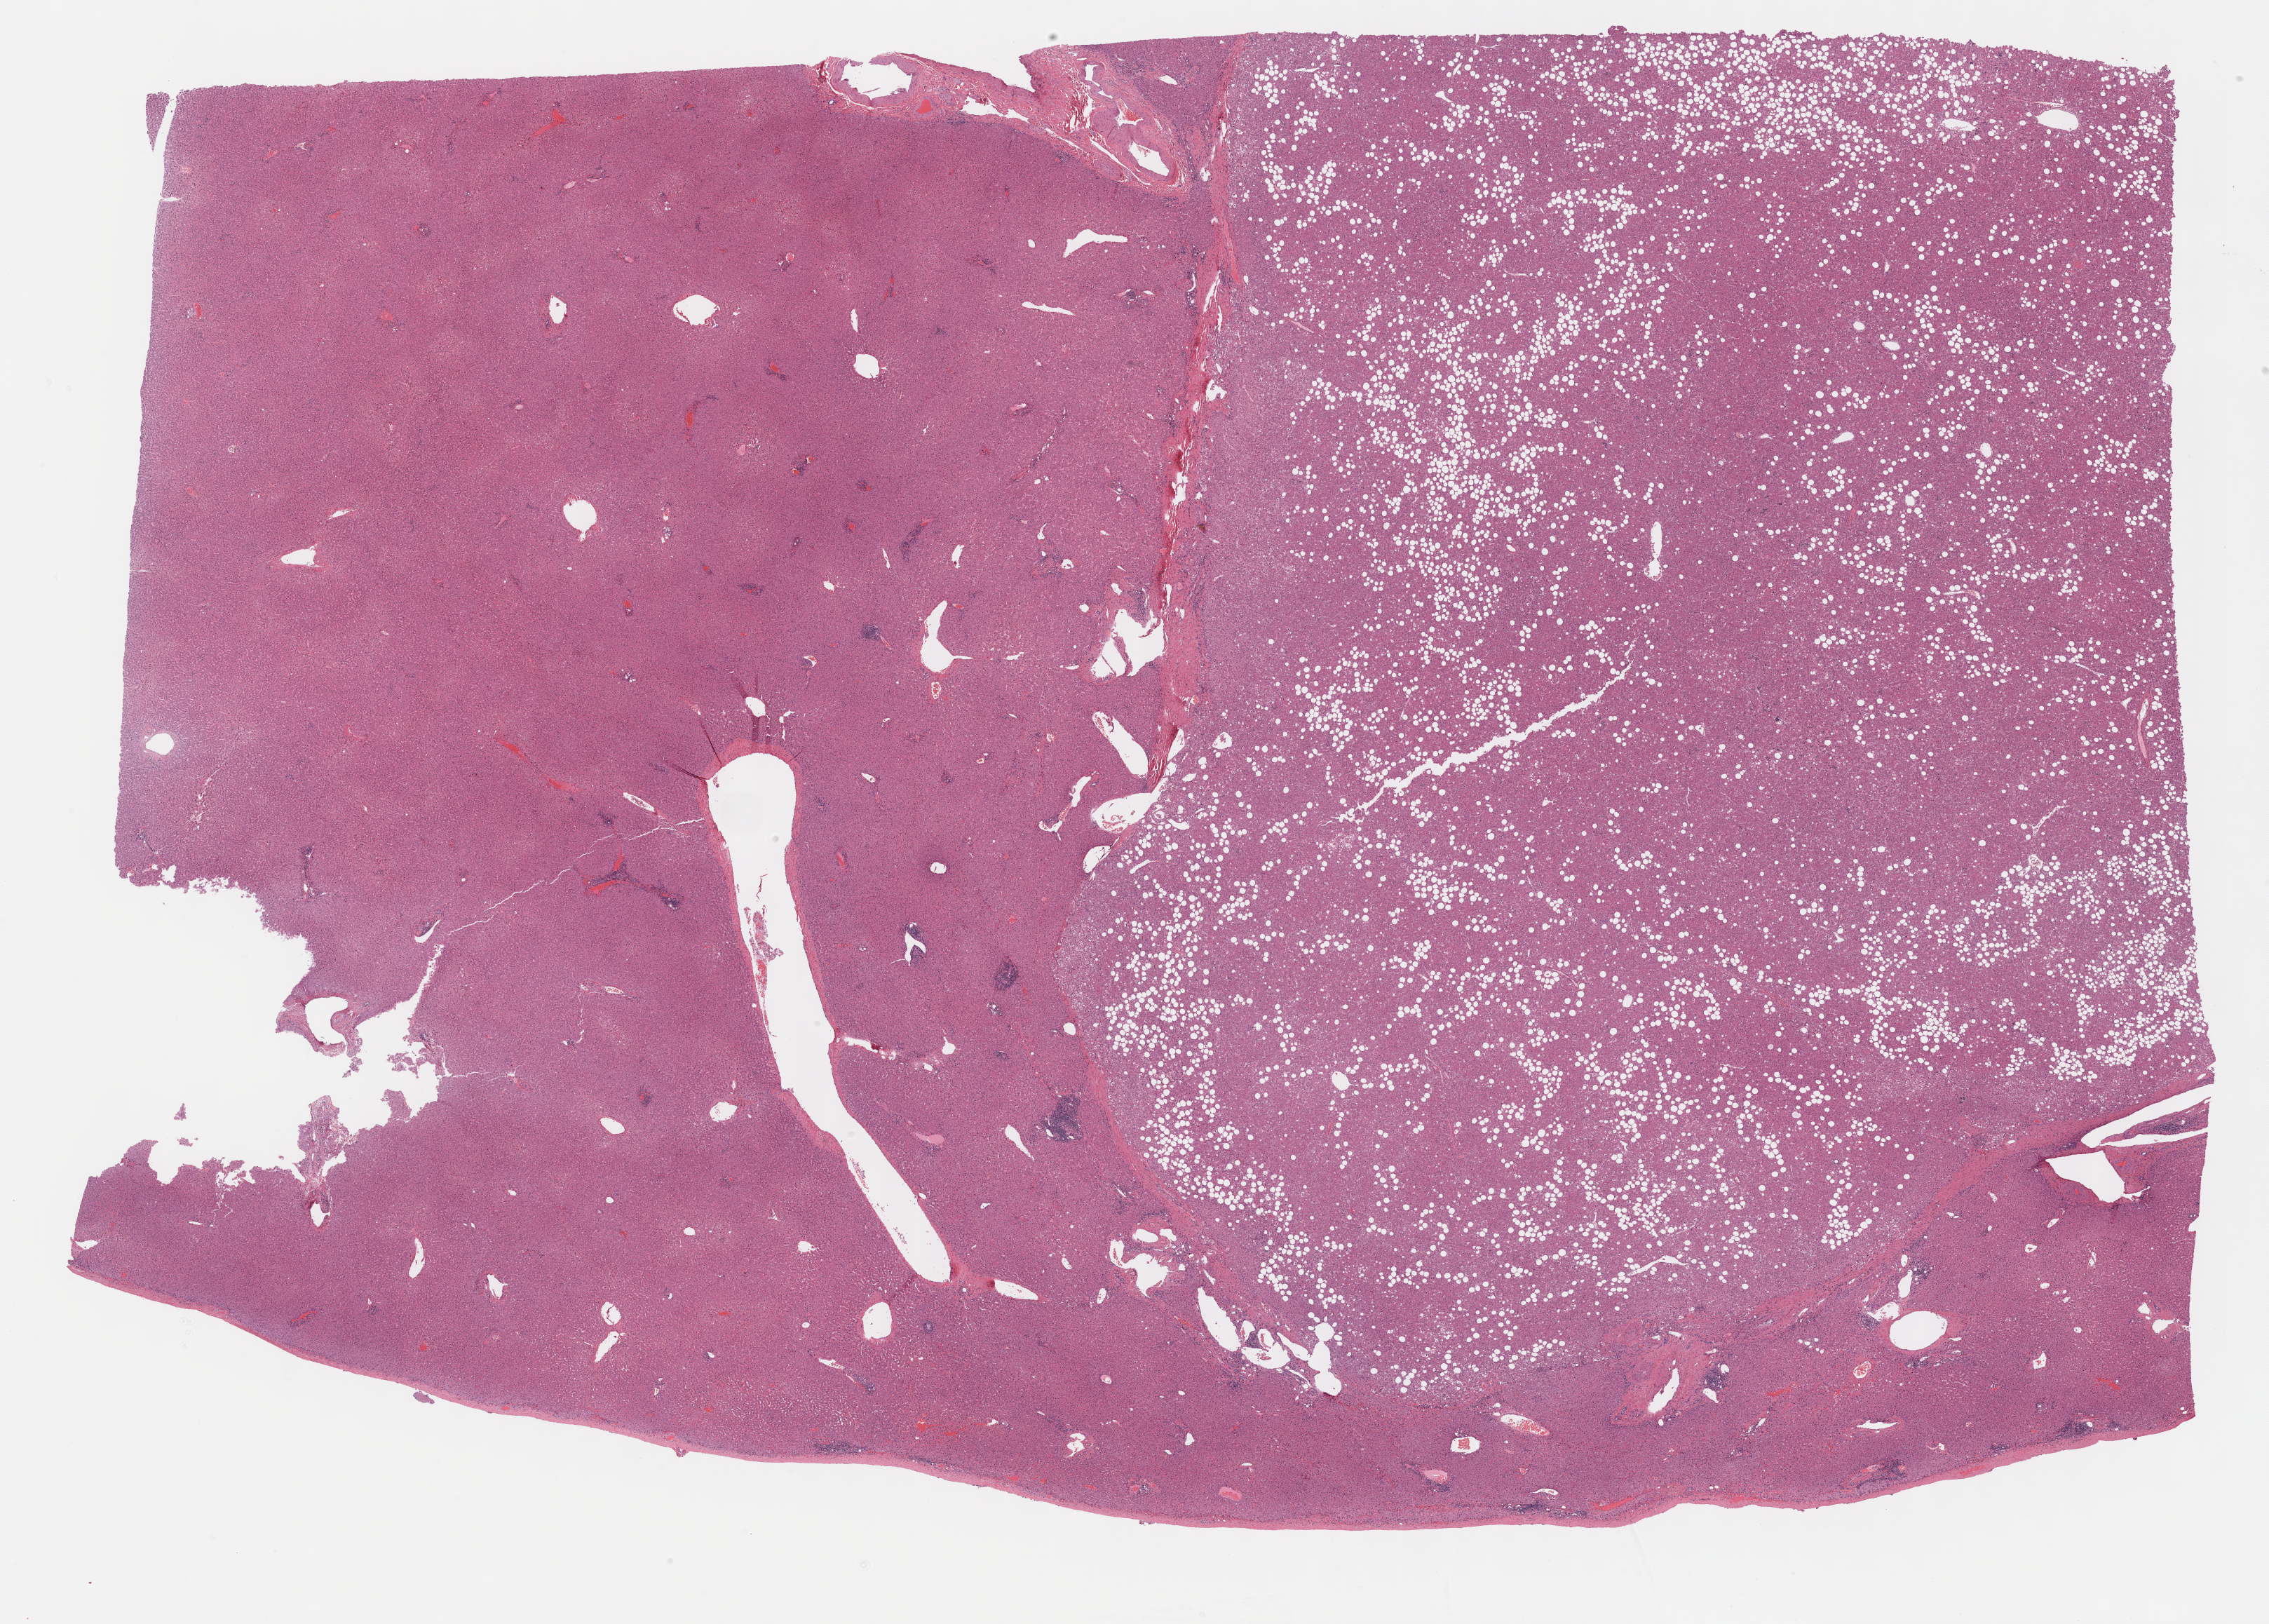
Digitized H&E tissue section (whole slide), shown as a low-resolution overview of the whole scanned area (about 26.2 x 18.7 mm, from a 40x scan); formalin-fixed paraffin-embedded (FFPE) diagnostic section; sample: primary tumour, liver. Male, age 71 years at initial diagnosis. Histologic grade: G2 (moderately differentiated).
Diagnosis: Hepatocellular carcinoma, NOS. AJCC pathologic stage: I (7th edition).